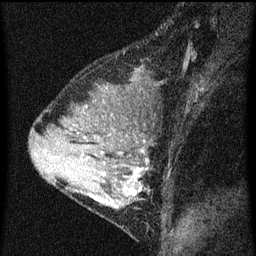
Breast MRI (dynamic contrast-enhanced), one sagittal slice. Position 26 of 60 along the scan axis. Dynamic contrast-enhanced series, image 2 of 3 at this slice position (ordered by acquisition). 1.5 T. TE 4.2 ms, TR 8 ms. 2 mm slice thickness. 256 × 256 image matrix, field of view 180 × 180 mm. Patient: female, 33 years.
Outlined on this slice (semi-automatically segmented with operator editing):
- analysis volume of interest (the breast-tissue region the enhancement analysis was run in; not a lesion): box from (x=67, y=118) to (x=155, y=213) px
- tumour enhancement mask (voxels above the 70 % enhancement threshold inside the analysis volume of interest): (x=88, y=140)–(x=149, y=201)